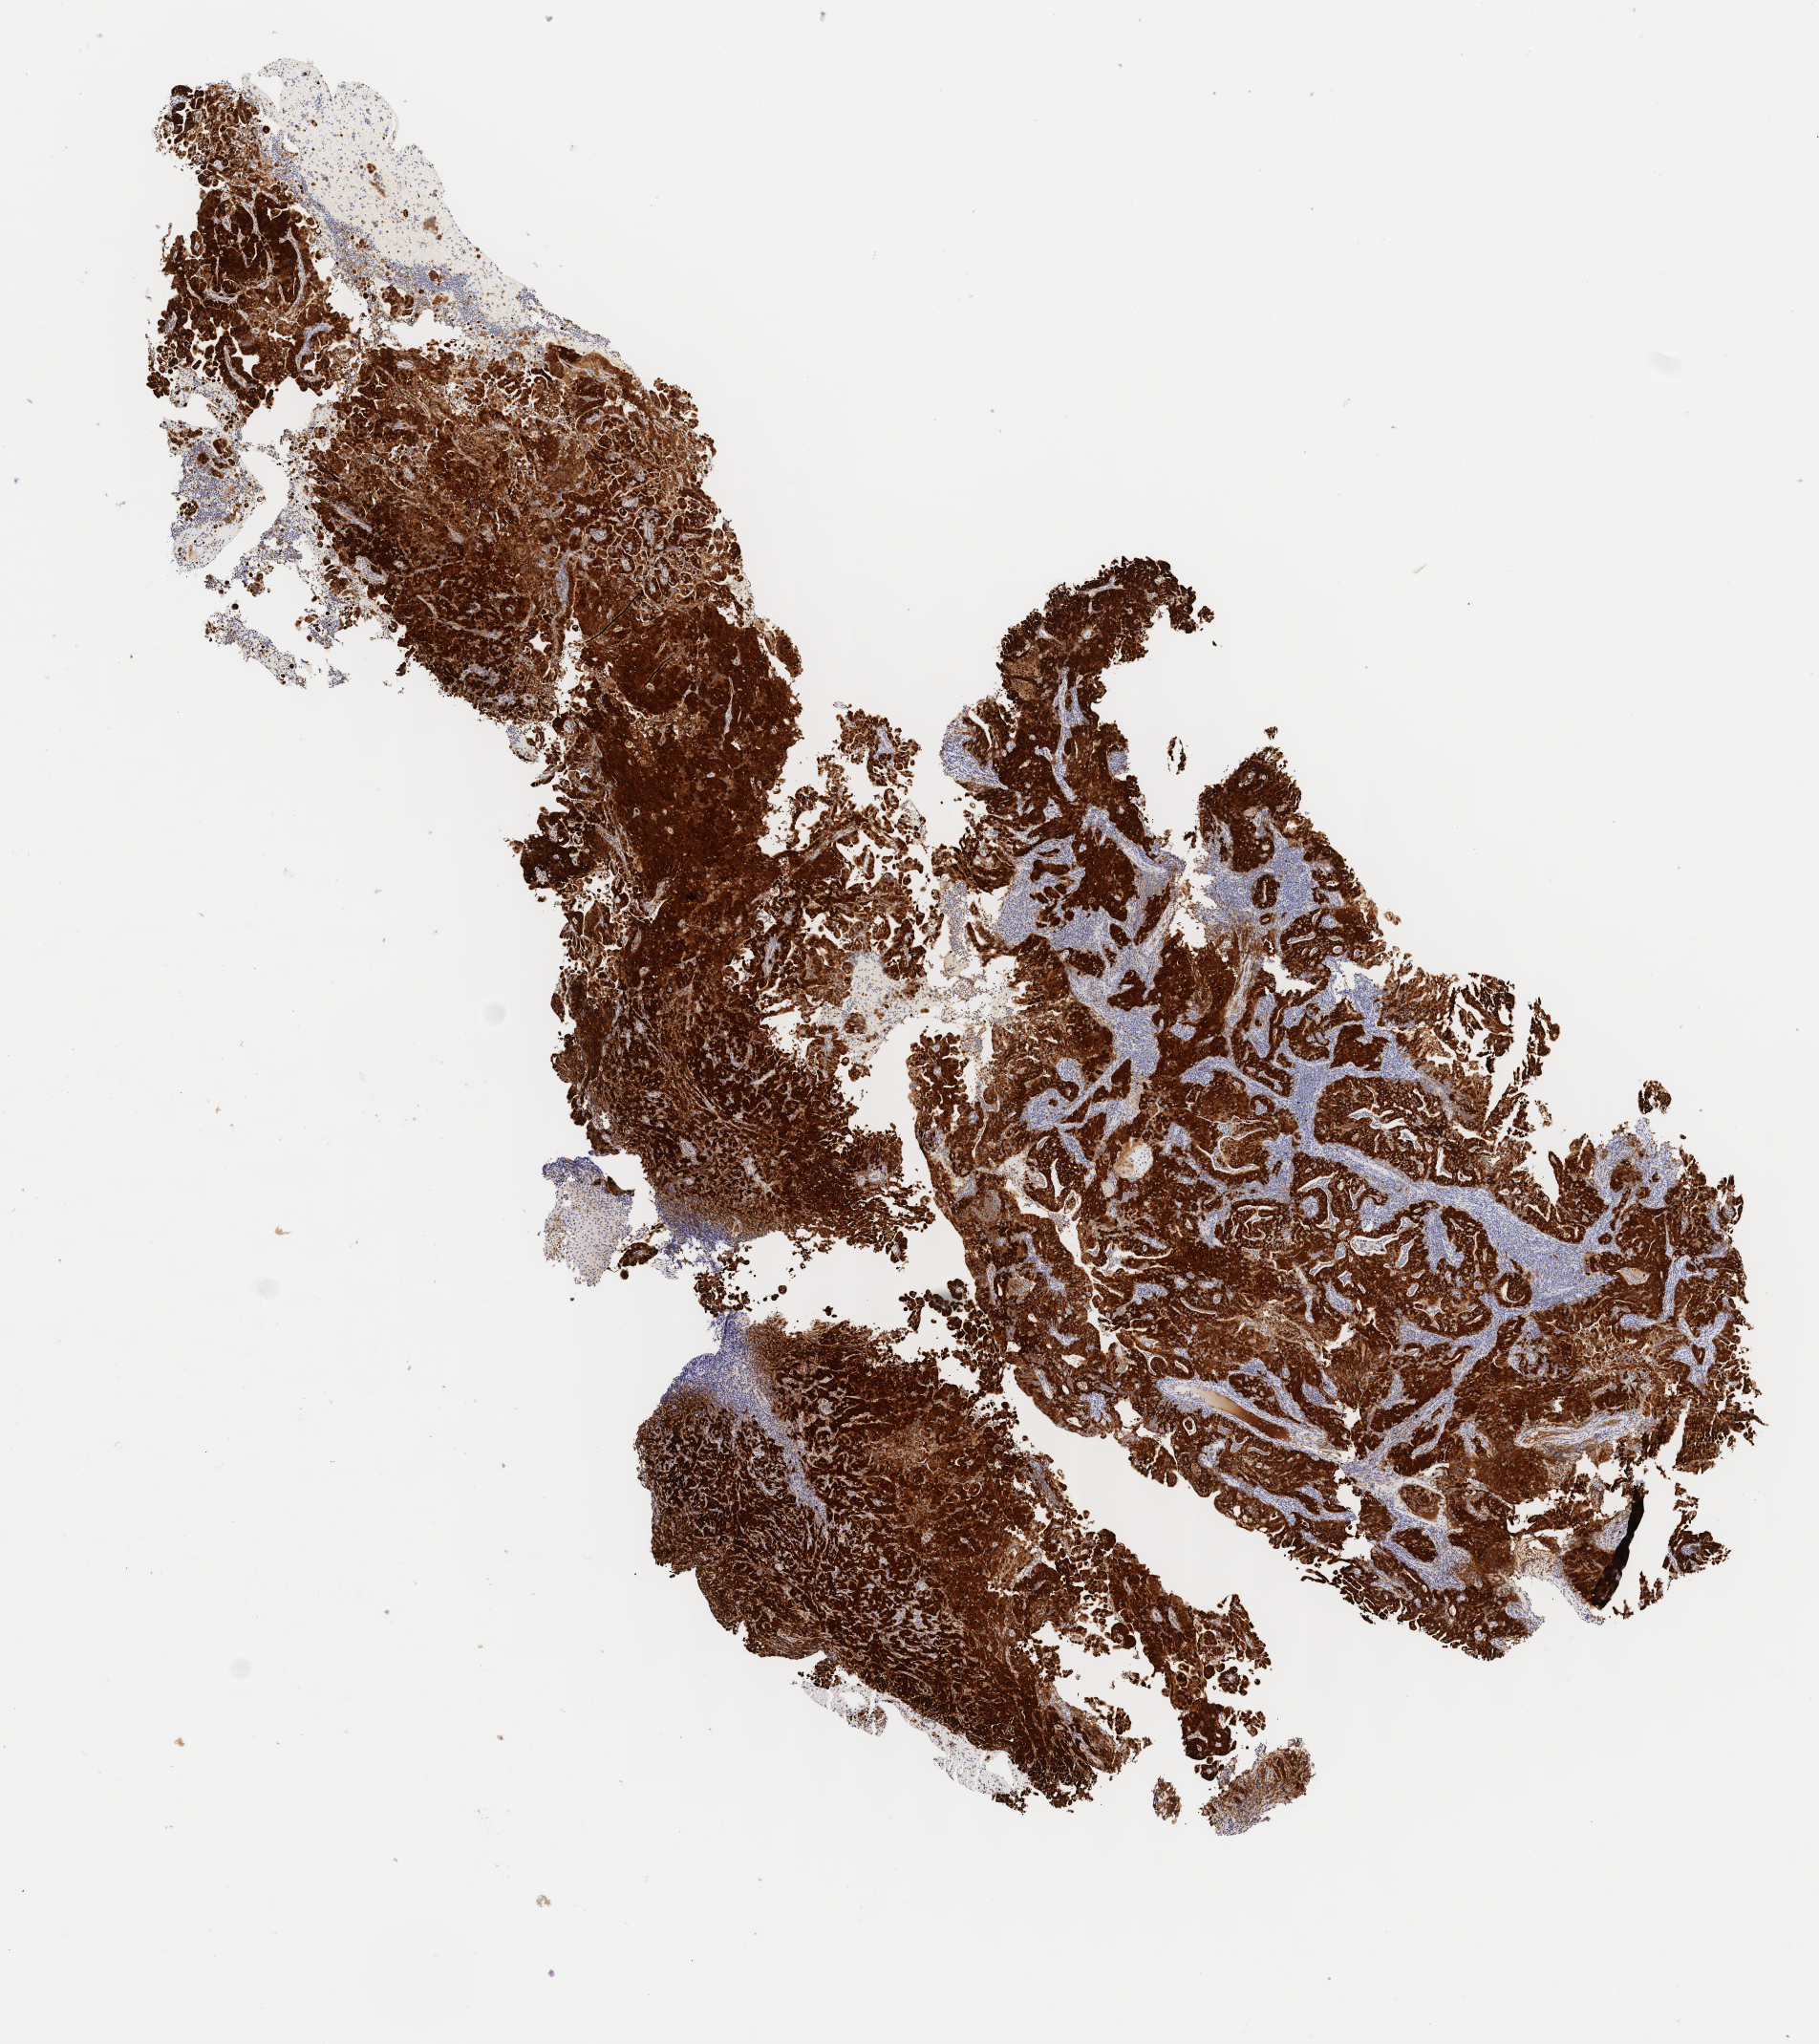
Whole-slide image, immunohistochemical stain for p16 (p16INK4a), low-resolution overview of the scanned area, about 7.6 x 8.5 mm. Tumor tissue. Site: cervix. Patient female; aged 57.
Diagnosis: Adenocarcinoma, NOS.